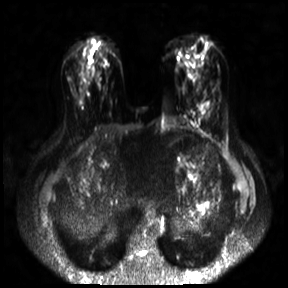
Breast MRI, one axial slice; position 12 of 30 along the scan axis; diffusion-weighted series; image 2 of 4 stored at this slice position (different b-values; order by instance number); 3 T; 4 mm slice thickness; 288 × 288 image matrix, field of view 360 × 360 mm. Female patient.
Annotated regions visible in this slice (outlined manually by an expert reader):
- tumour on diffusion-weighted imaging: bounding box [x1, y1, x2, y2] px = [199, 101, 210, 114]